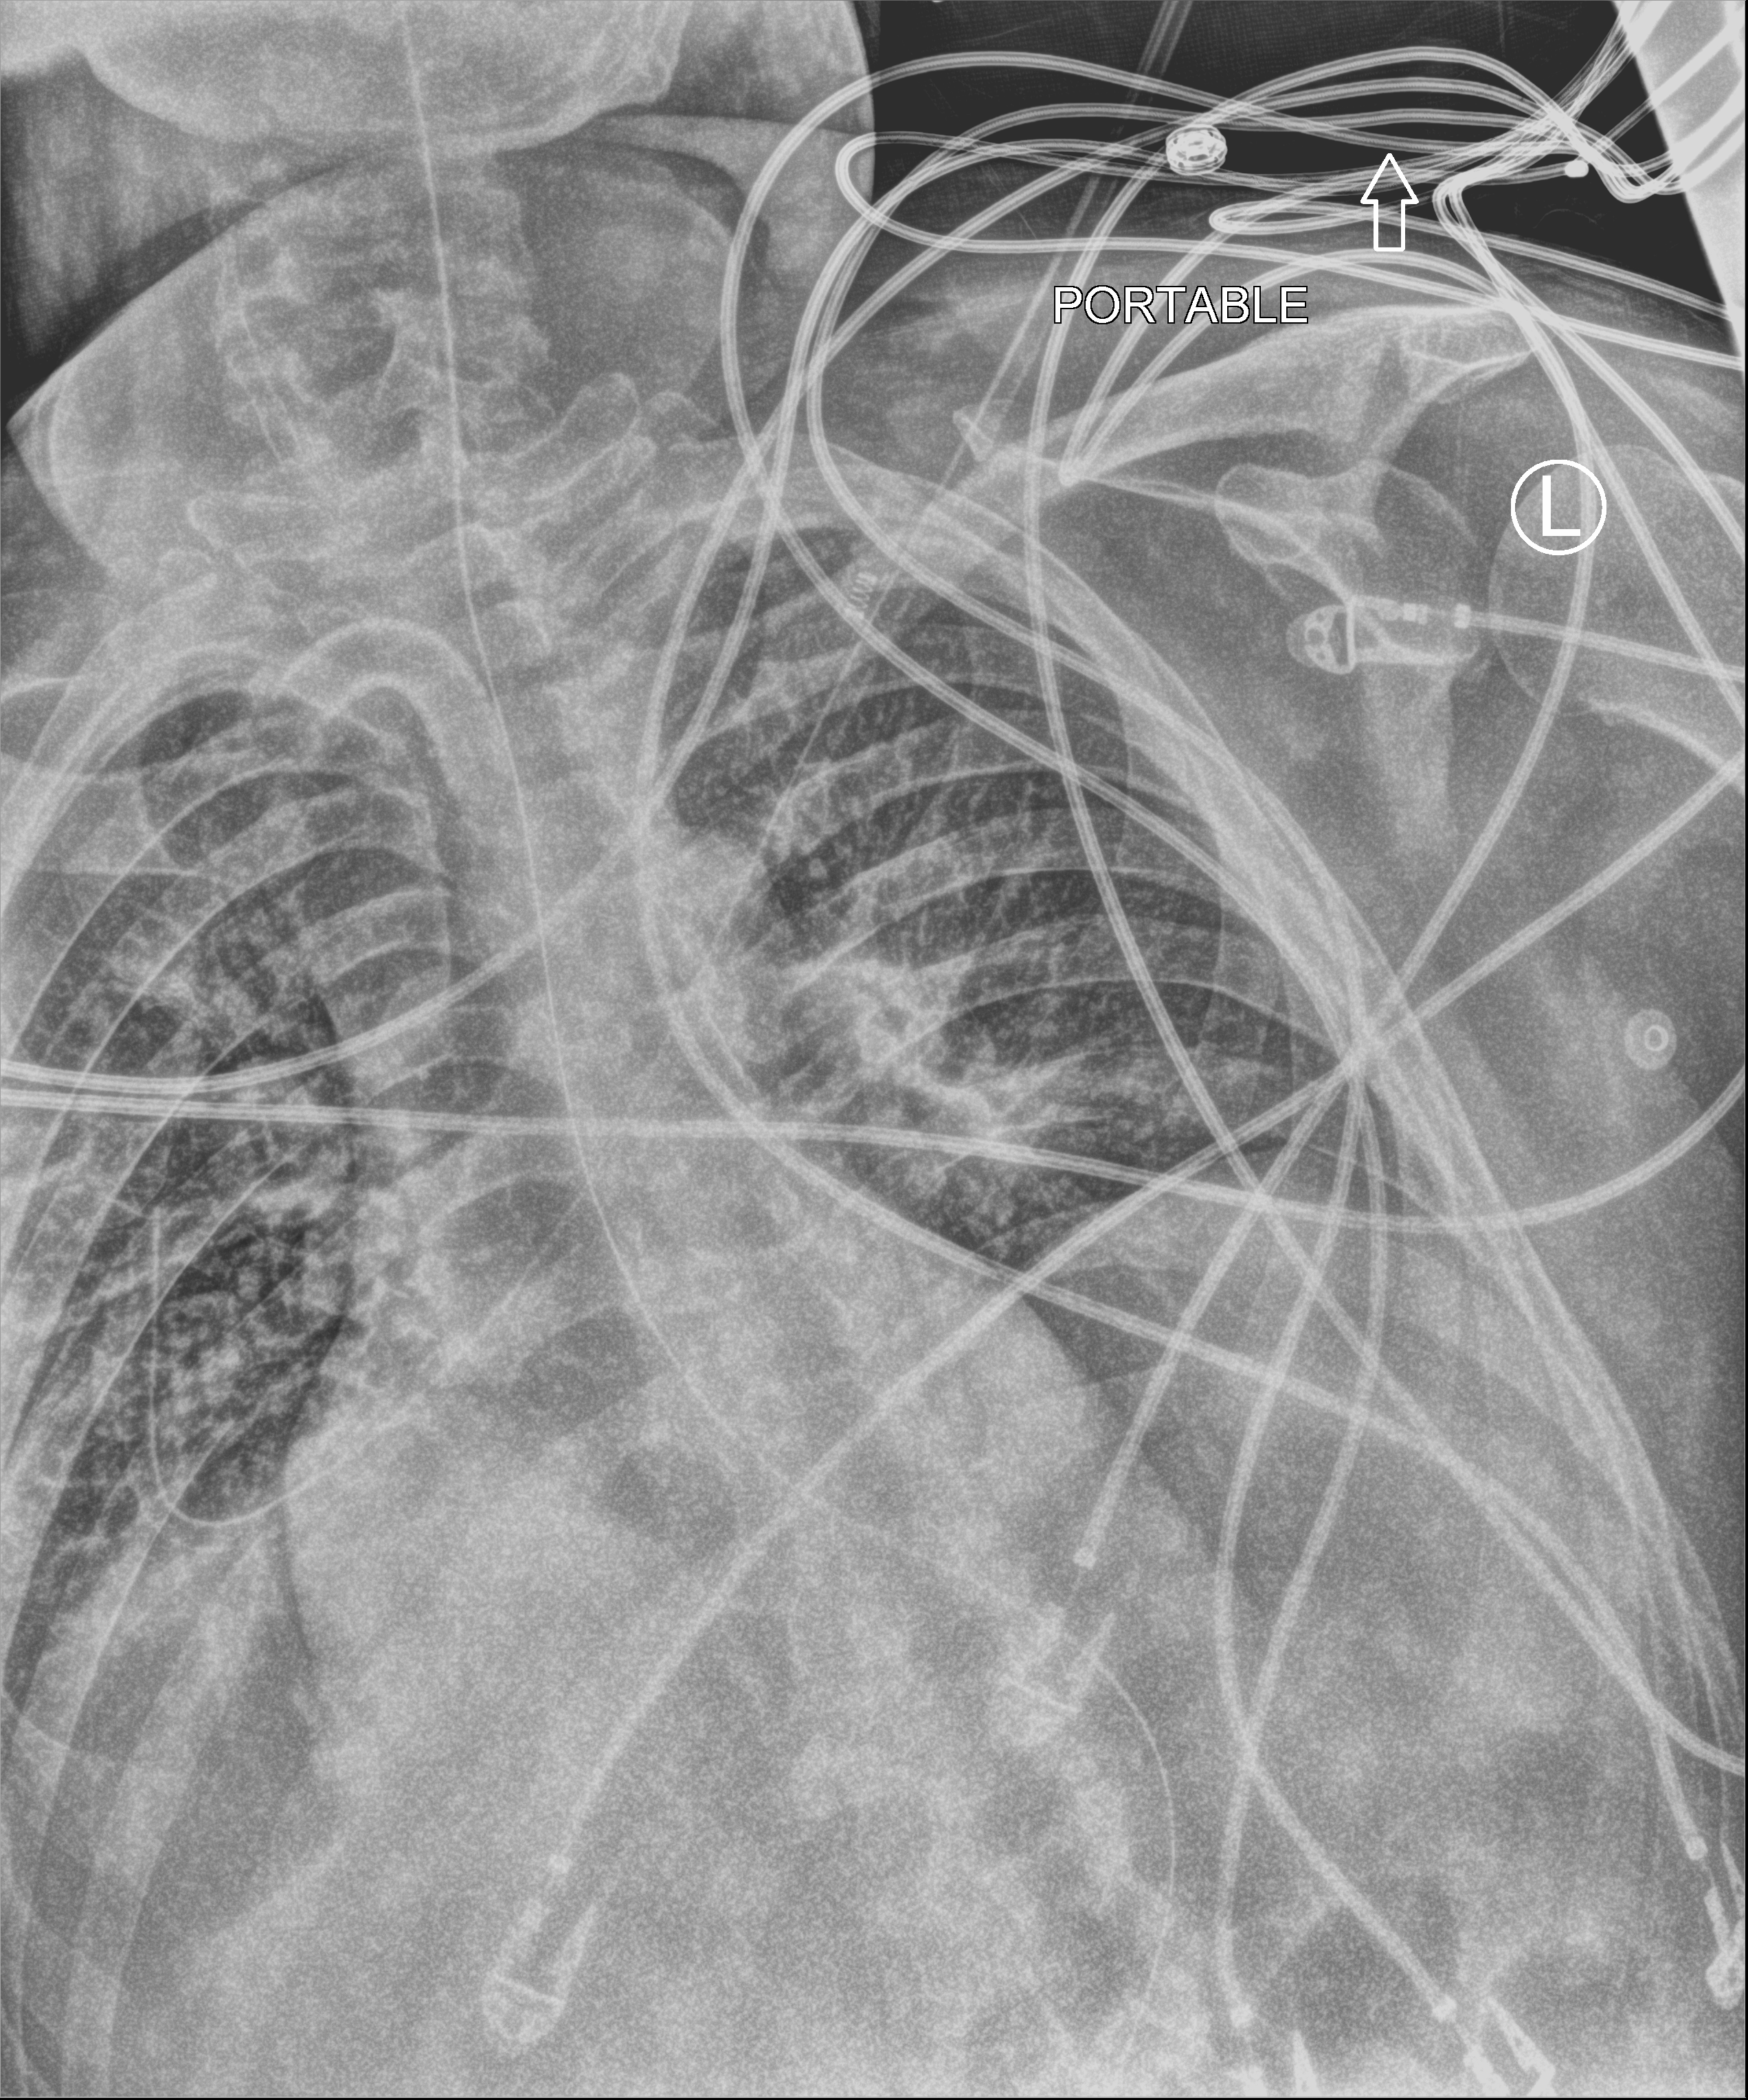
Chest X-ray (portable), anteroposterior (AP) projection. Patient hospitalised with COVID-19; male, aged 18–59 years.
Admission-level facts for this patient (not findings on this image; timing relative to this image not recorded): mechanically ventilated during this hospital stay: yes; admitted to intensive care during this hospital stay: yes.